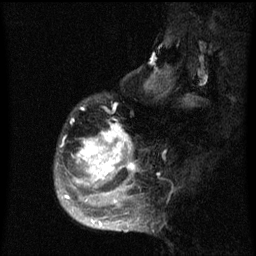
Breast MRI (dynamic contrast-enhanced), one sagittal slice. Position 17 of 60 along the scan axis. Dynamic contrast-enhanced series, image 2 of 3 at this slice position (ordered by acquisition). 1.5 T. TE 4.2 ms, TR 8 ms. 256 × 256 image matrix, field of view 190 × 190 mm. Patient: female, 50 years.
Annotated regions visible in this slice (semi-automatic segmentation, software-assisted and operator-edited):
- analysis volume of interest (the breast-tissue region the enhancement analysis was run in; not a lesion): bounding box (x1, y1, x2, y2) in pixels: (55, 97, 142, 216)
- tumour enhancement mask (voxels above the 70 % enhancement threshold inside the analysis volume of interest): (65, 123, 135, 201)